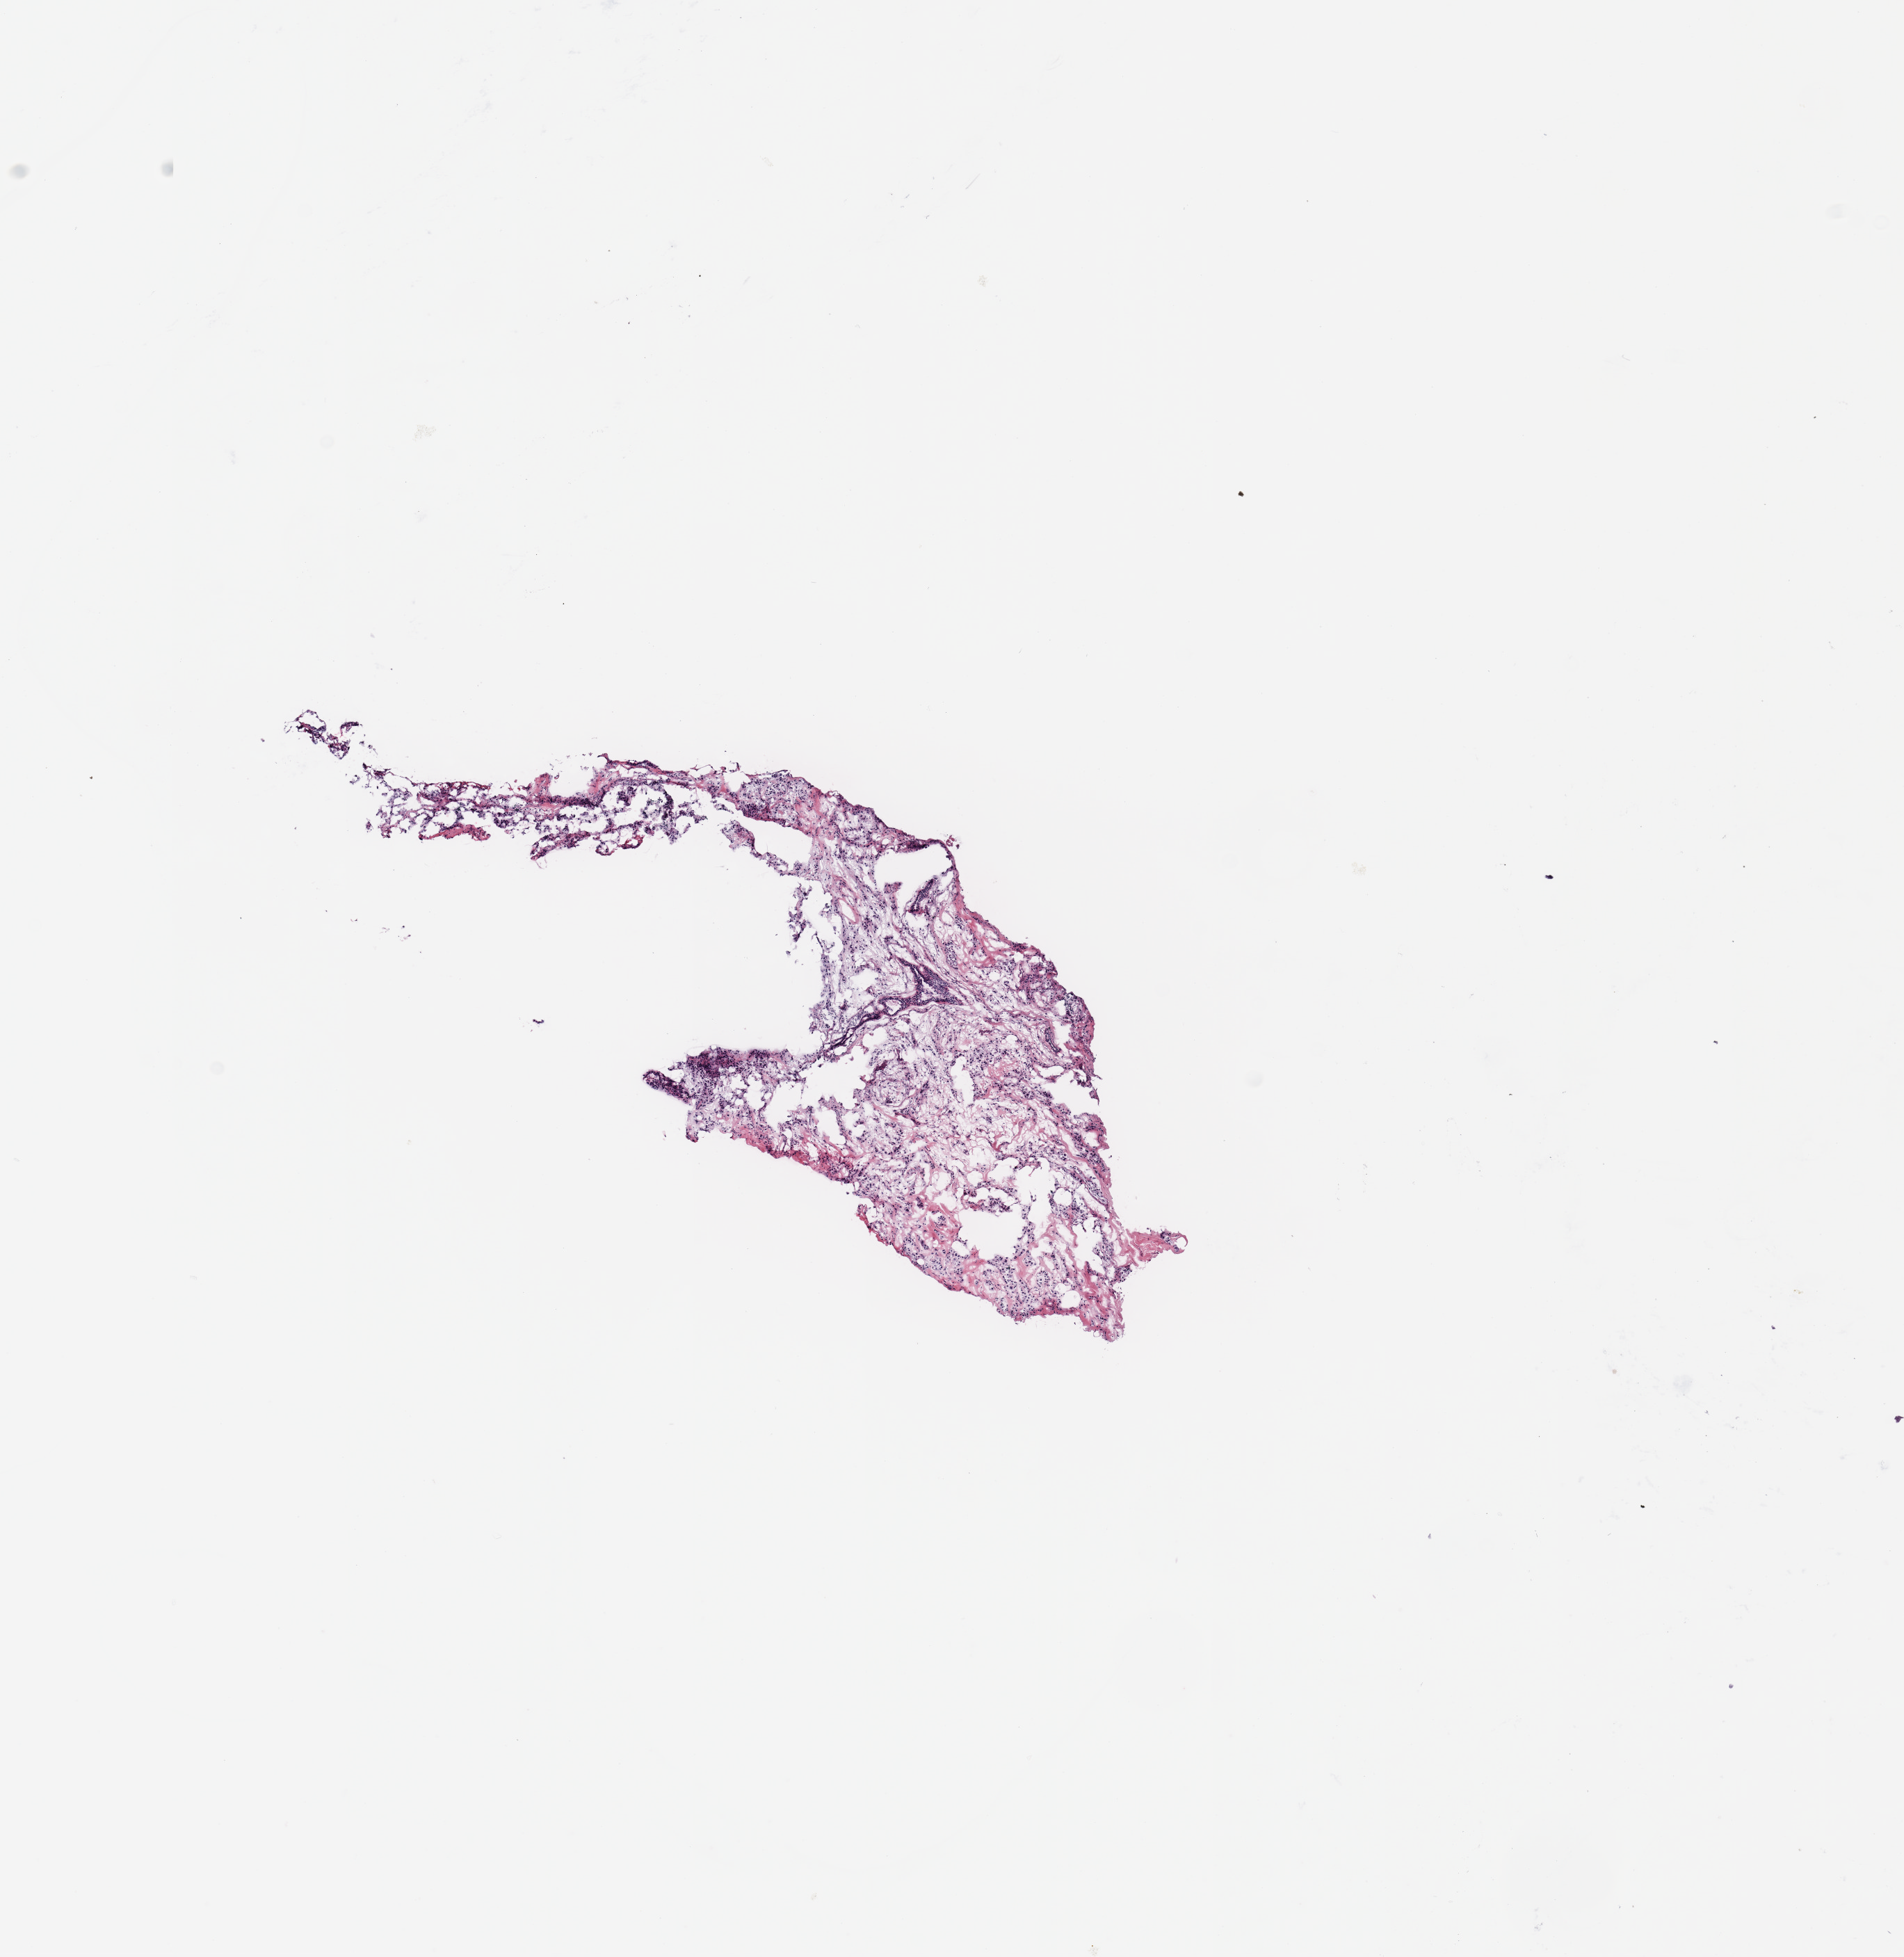
Whole-slide histology image, Hematoxylin and eosin (H&E) stained — low-resolution overview of the scanned area, about 10.8 x 11.1 mm. Breast, tissue type not recorded.
* patient diagnosis (cohort enrolment): breast cancer (breast)